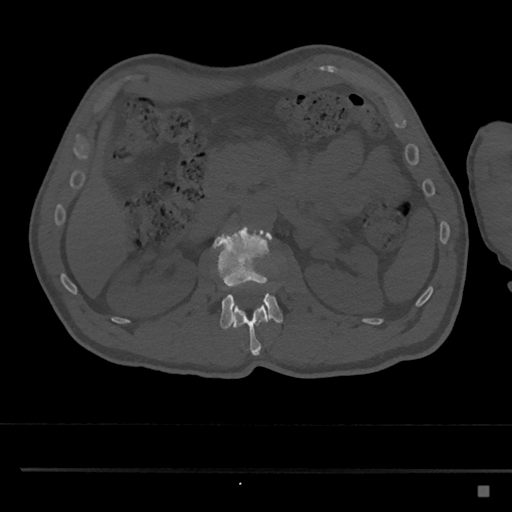
CT including the spine, one axial slice. Slice 792 of 797 in the series (ordered by position). 120 kVp. Bone window (W 1800 / L 400 HU). 0.5 mm slice thickness. 512 × 512 image matrix, field of view 391 × 391 mm. Male patient, age 59 years. Case-level facts recorded for this patient, not image findings: primary cancer: prostate.
Outlined on this slice (semi-automatically segmented with operator editing):
- L1 vertebra: bounding box <233,301,269,356> (left, top, right, bottom; pixels)
- L2 vertebra: <209,226,283,330>